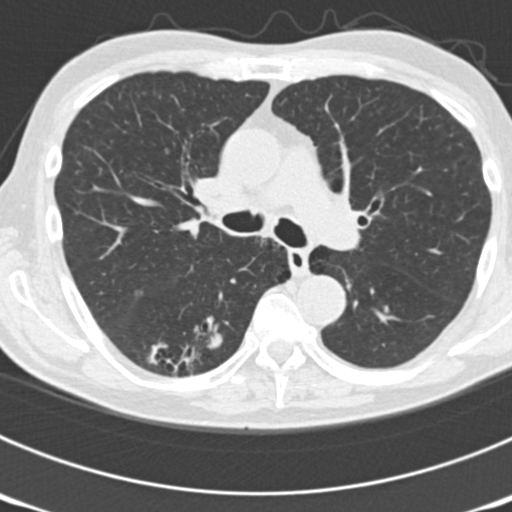
Low-dose screening chest CT, one axial slice. Slice 115 of 177 in the series (ordered by position). Lung window (W 1500 / L -600 HU). 512 × 512 image matrix.
Outlined on this slice (outlined manually by an expert reader):
- lesion 6 (nodule, lower lobe of right lung): bounding box [x1, y1, x2, y2] px = [204, 331, 222, 350]